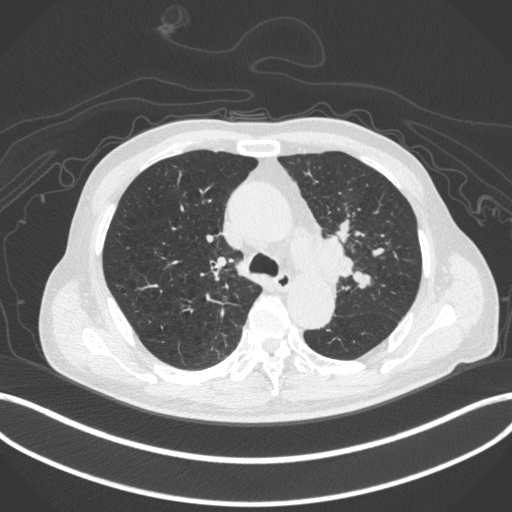
Chest CT, one axial slice. Position 297 of 420 along the scan axis. 120 kVp. Lung window (W 1500 / L -600 HU). 1 mm slice thickness. 512 × 512 image matrix, field of view 400 × 400 mm. Patient: male, 77 years. Case-level facts recorded for this patient, not image findings: clinical TNM (as recorded): T3 N1 M0.
Annotated regions visible in this slice (rectangle marked by the reading radiologist):
- lung tumour (recorded histology: adenocarcinoma): bounding box <308,234,359,287> (left, top, right, bottom; pixels)